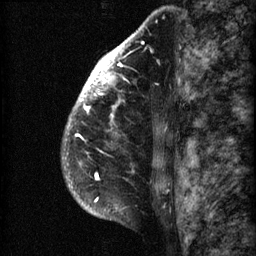
Breast MRI (dynamic contrast-enhanced), one sagittal slice. Position 50 of 60 along the scan axis. 3 images stored at this slice position (order not interpretable as contrast timing). 1.5 T. TE 4.2 ms, TR 22.7 ms. 256 × 256 image matrix, field of view 180 × 180 mm. Female patient, age 48 years. From the clinical record (not read from this slice): setting: breast cancer imaged before/during neoadjuvant chemotherapy; receptor status: triple-negative.
Outlined on this slice (semi-automatically segmented with operator editing):
- analysis volume of interest (the breast-tissue region the enhancement analysis was run in; not a lesion): bounding box [x1, y1, x2, y2] px = [61, 30, 173, 207]
- tumour enhancement mask (voxels above the 90 % enhancement threshold inside the analysis volume of interest): [62, 31, 140, 202]